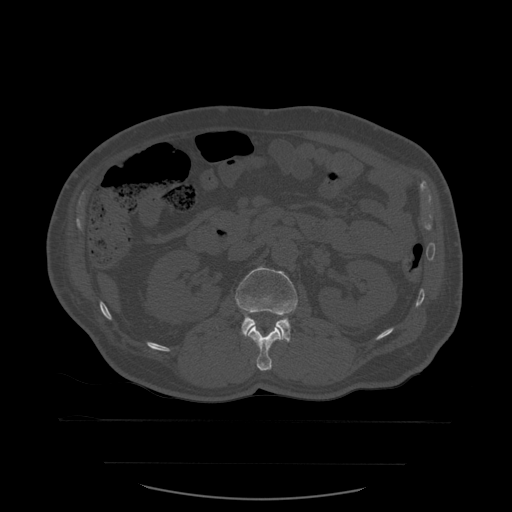
CT including the spine, one axial slice; position 231 of 590 along the scan axis; bone window (W 1800 / L 400 HU); 1.25 mm slice thickness; 512 × 512 image matrix. Patient age 71 years. From the clinical record (not read from this slice): primary cancer: lung.
Structures marked on this image (semi-automatic segmentation, software-assisted and operator-edited):
- L1 vertebra: box from (x=248, y=325) to (x=282, y=371) px
- L2 vertebra: (x=235, y=267)–(x=298, y=343)